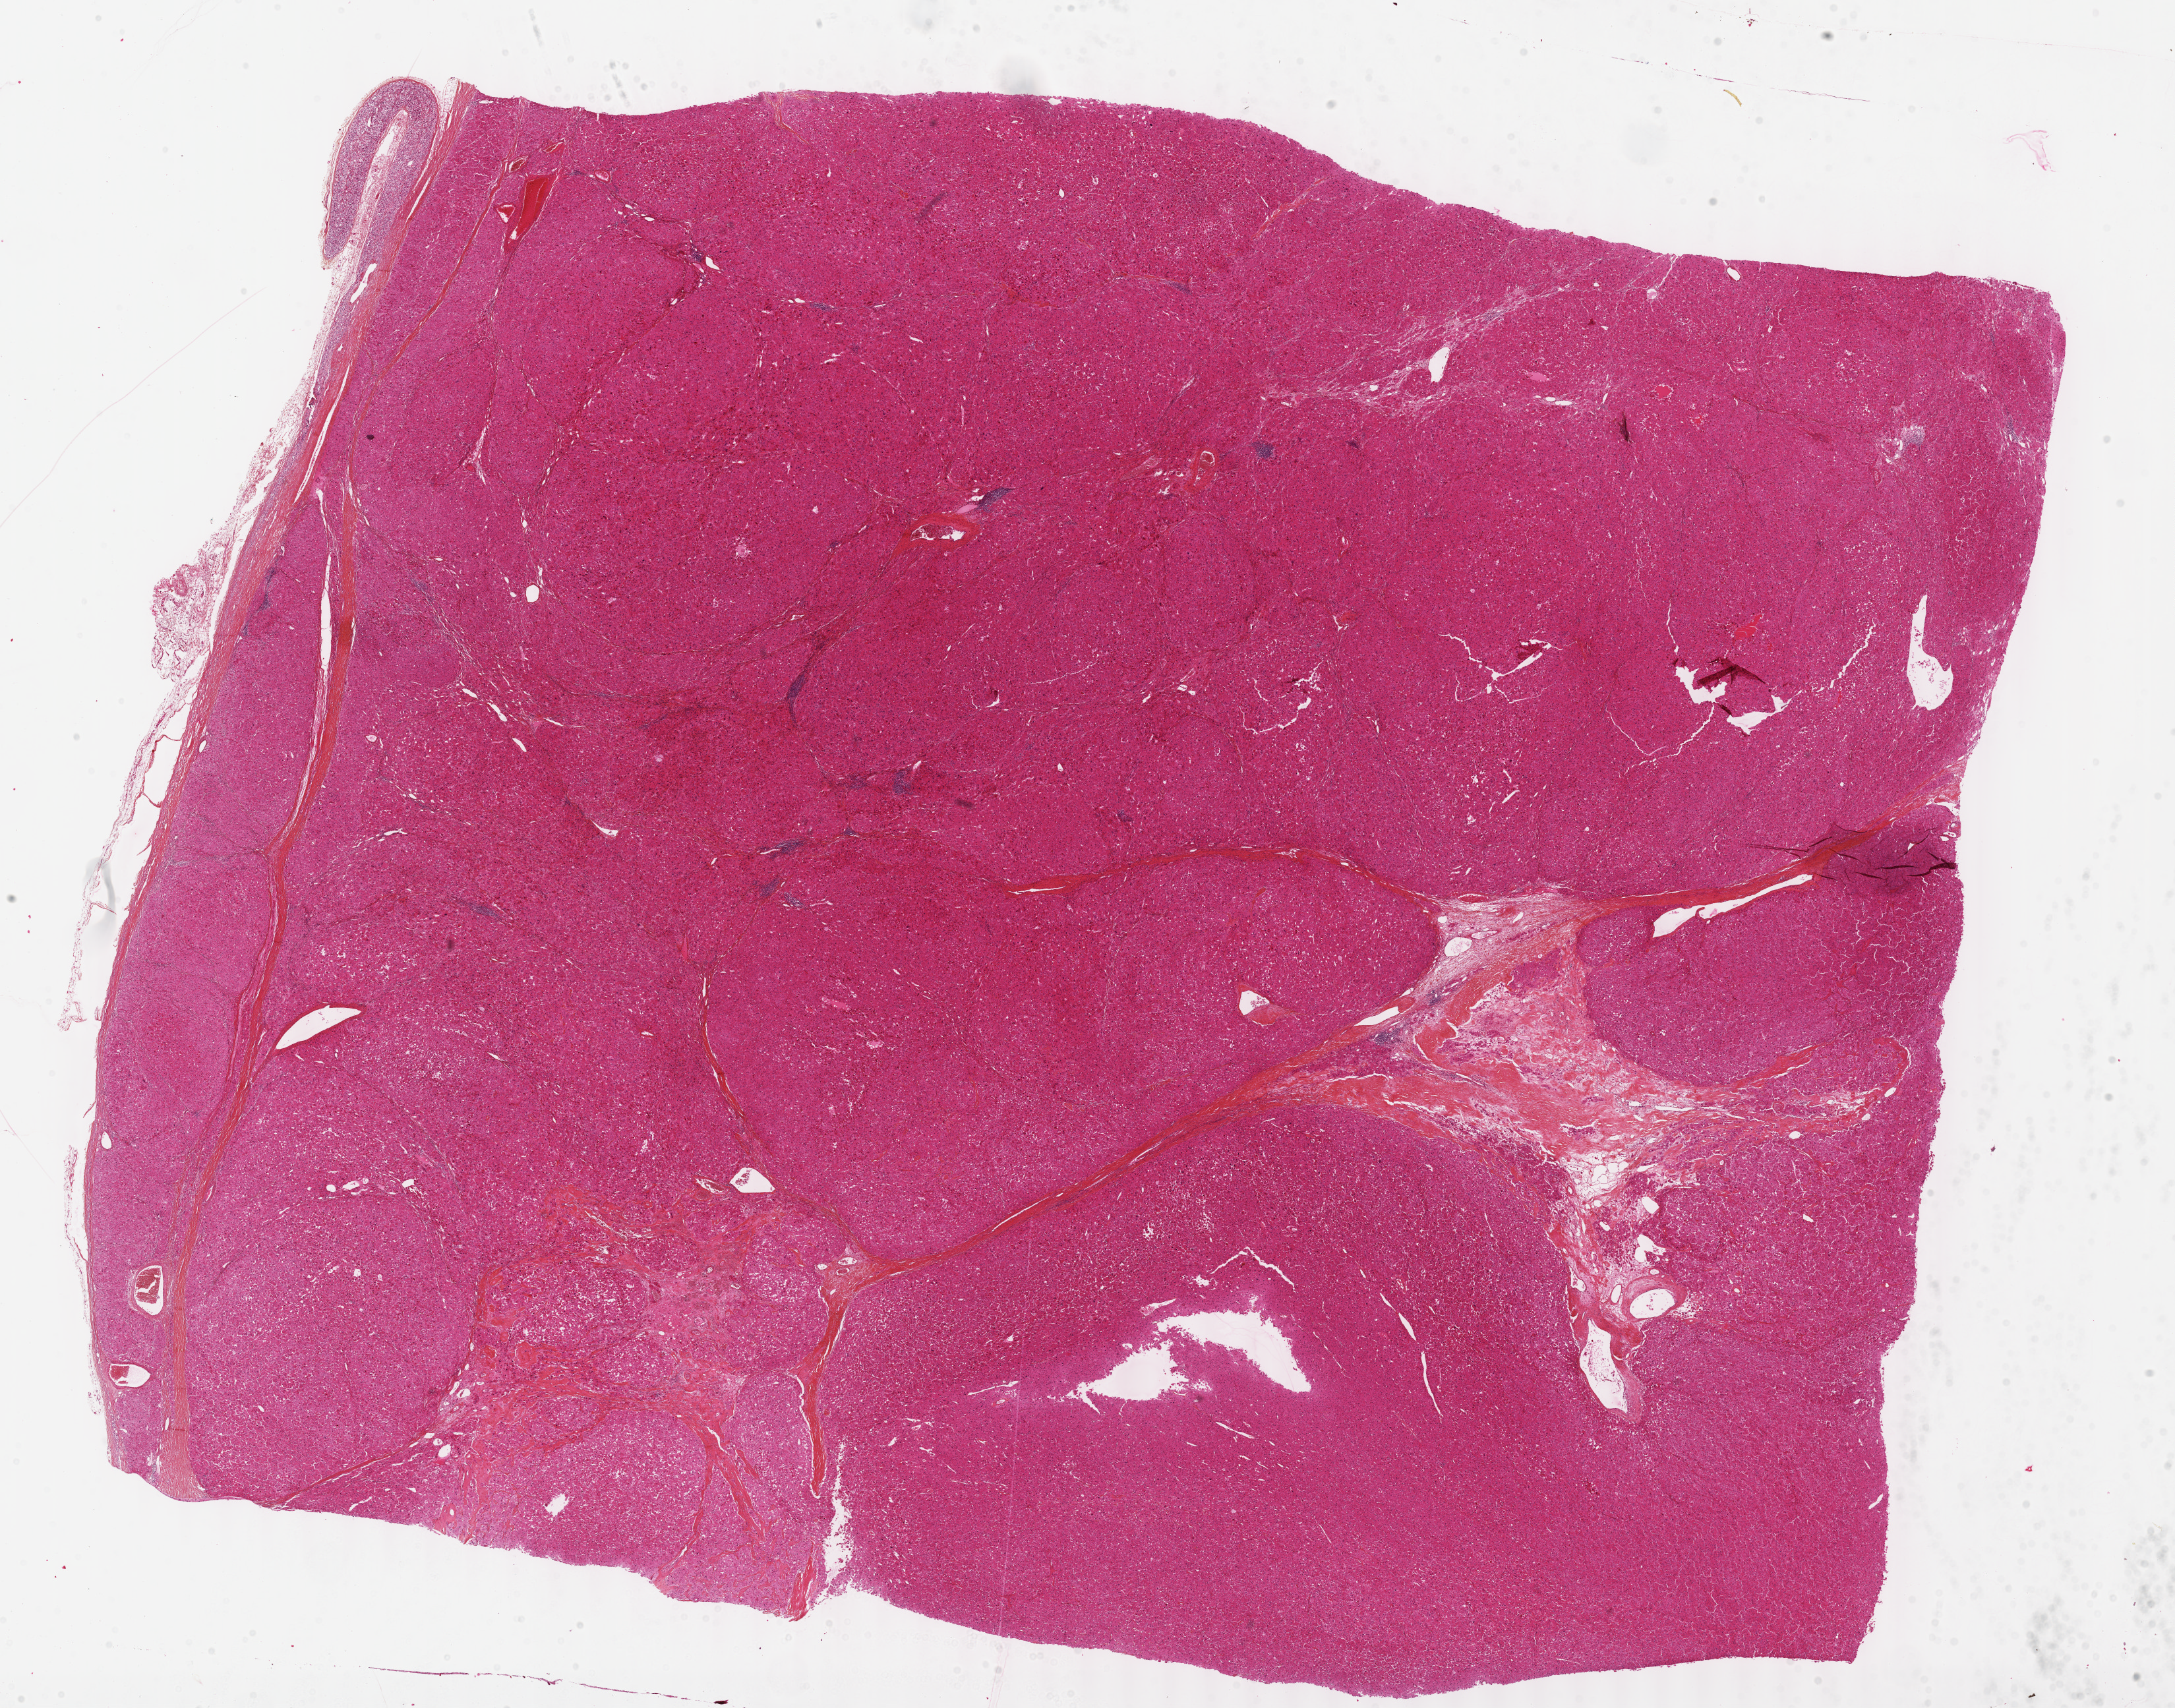
Whole-slide histology image, H&E, low-resolution overview of the scanned area, about 26.7 x 20.9 mm; formalin-fixed paraffin-embedded (FFPE) diagnostic section; primary tumour sample from the adrenal cortex. Female patient; age at initial diagnosis 37 years.
• lymph nodes positive (case pathology): 0 of 21 examined
• diagnosis: Adrenal cortical carcinoma (cortex of adrenal gland)